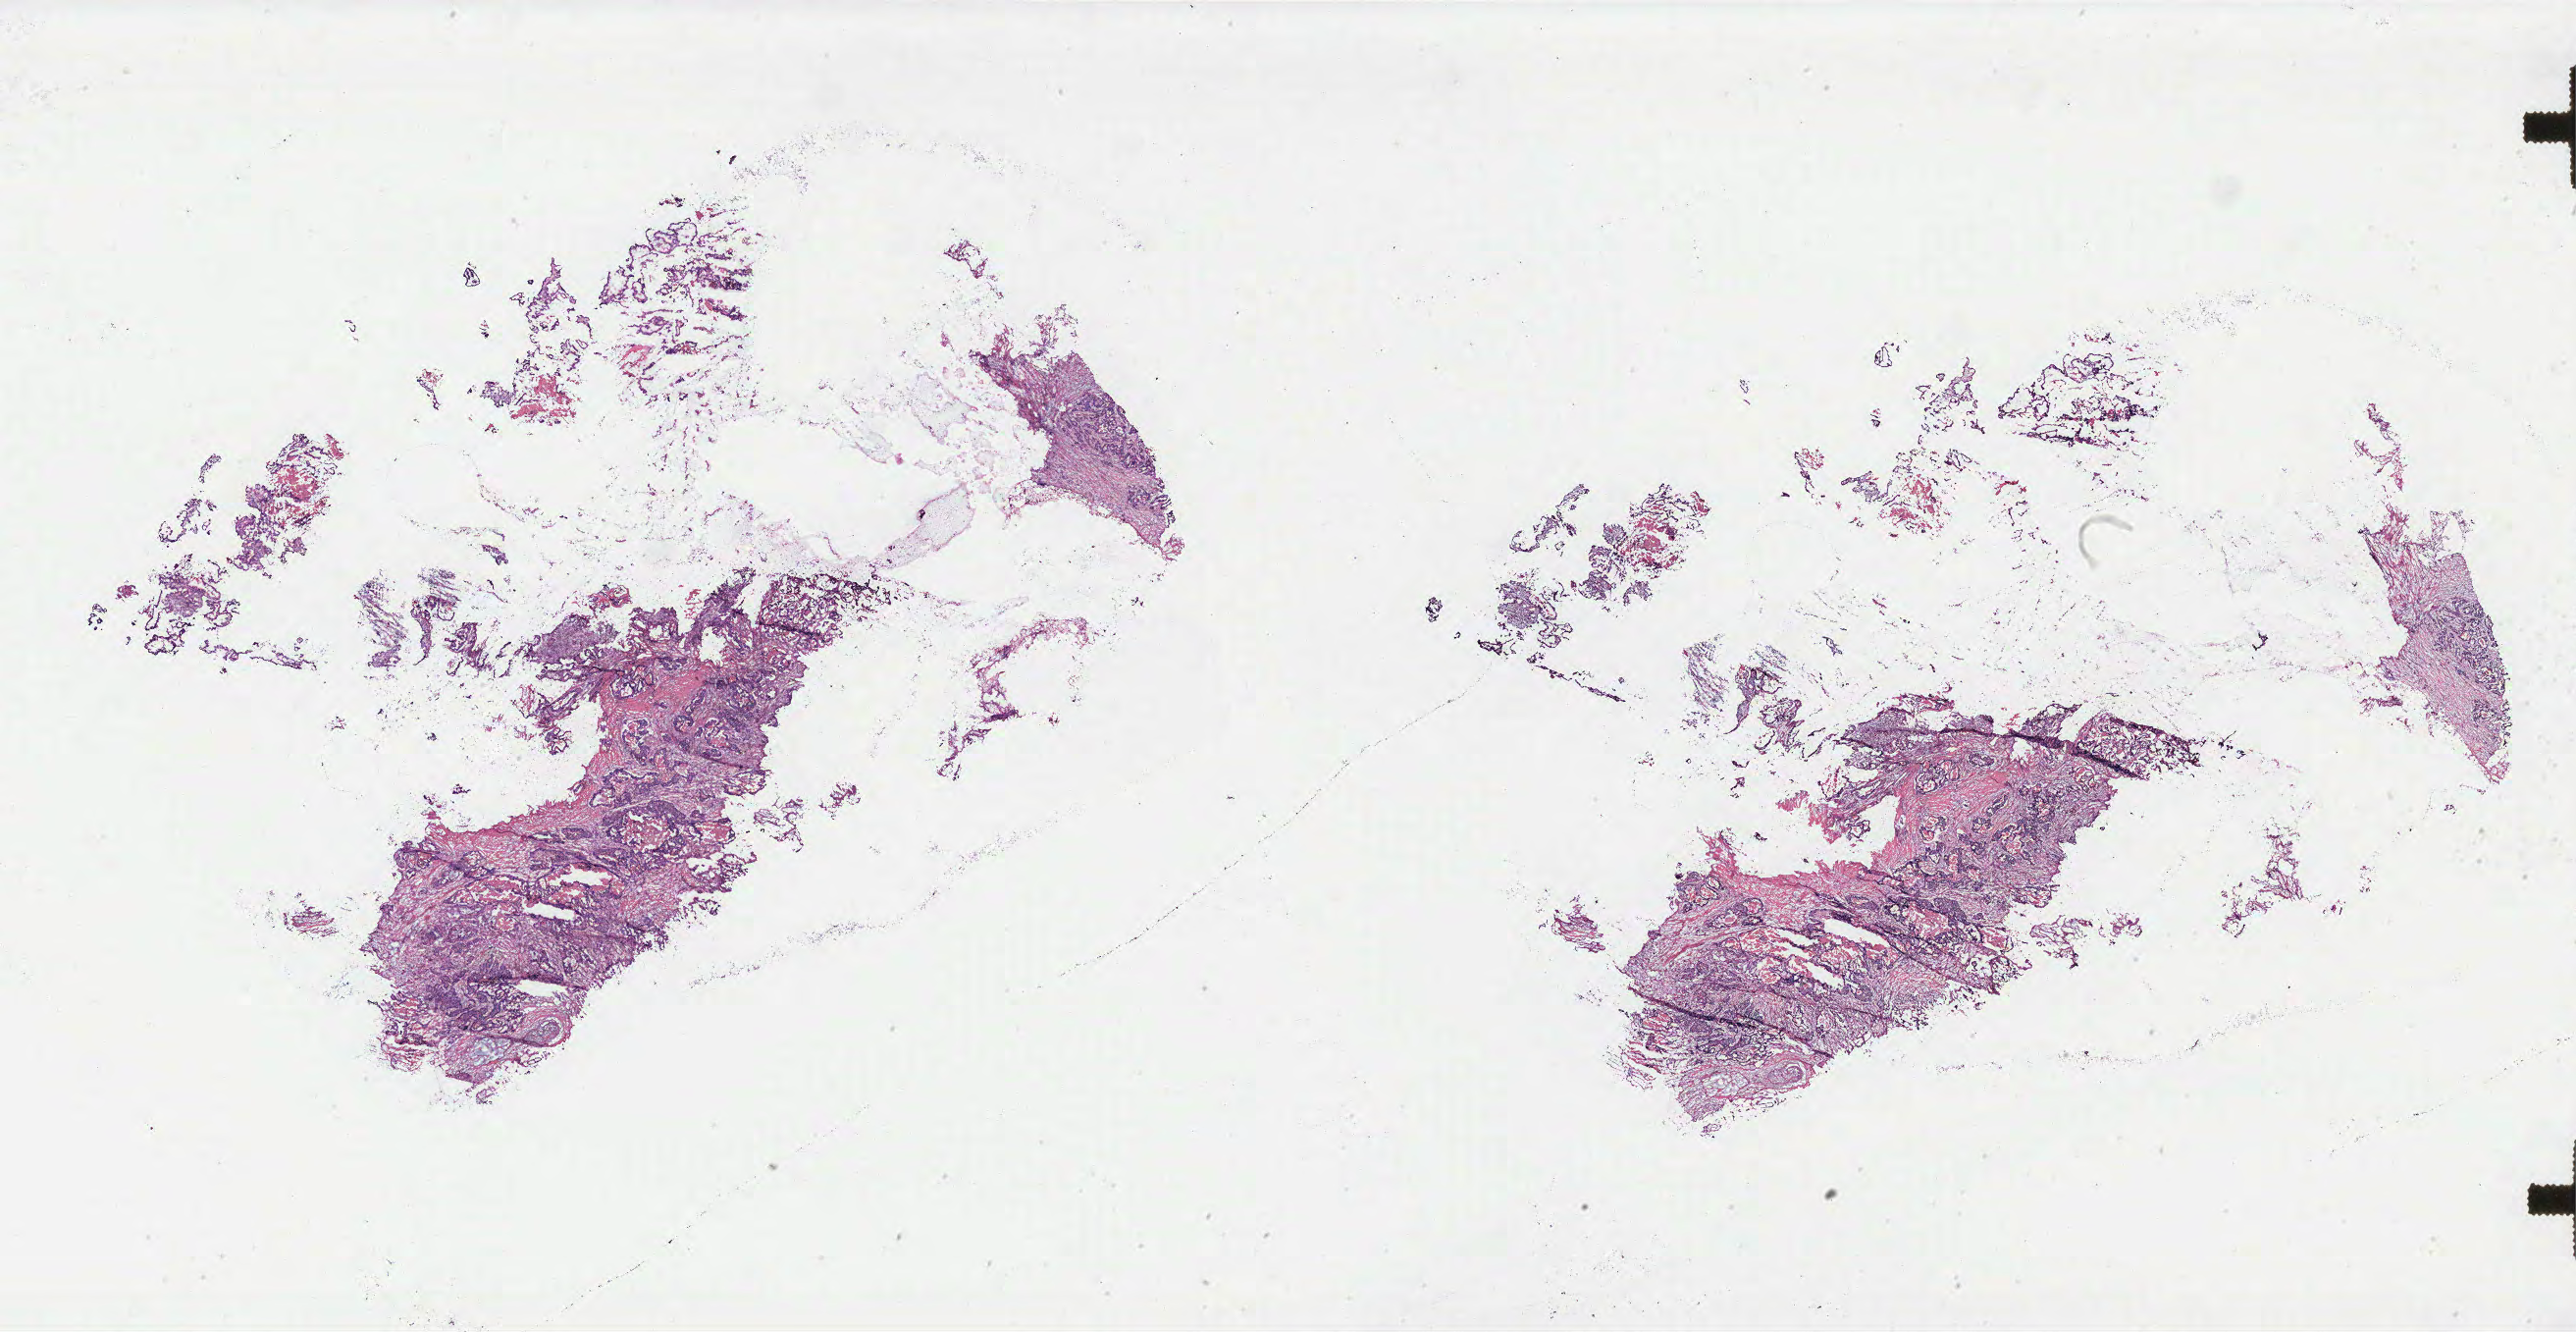
Hematoxylin and eosin (H&E) stained whole-slide image, whole scanned area (about 42.0 x 21.7 mm) shown as a low-resolution overview. Colon, normal (non-tumour) tissue. 74-year-old female patient.
This section: normal (non-tumour) tissue from the same patient. Patient diagnosis: Adenocarcinoma, NOS.